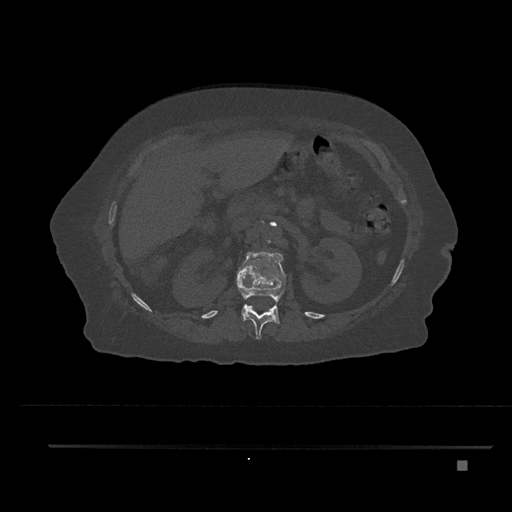
CT including the spine, one axial slice; reconstruction kernel Br40s/3; bone window (W 1800 / L 400 HU); 0.5 mm slice thickness; 512 × 512 image matrix, field of view 437 × 437 mm. Patient: female, 76 years. Case-level facts recorded for this patient, not image findings: primary cancer: lung; vertebrae with lytic lesions (as recorded): T11, L3.
Structures marked on this image (semi-automatically segmented with operator editing):
- L1 vertebra: bounding box [x1, y1, x2, y2] px = [236, 250, 286, 324]
- T12 vertebra: [246, 306, 275, 339]